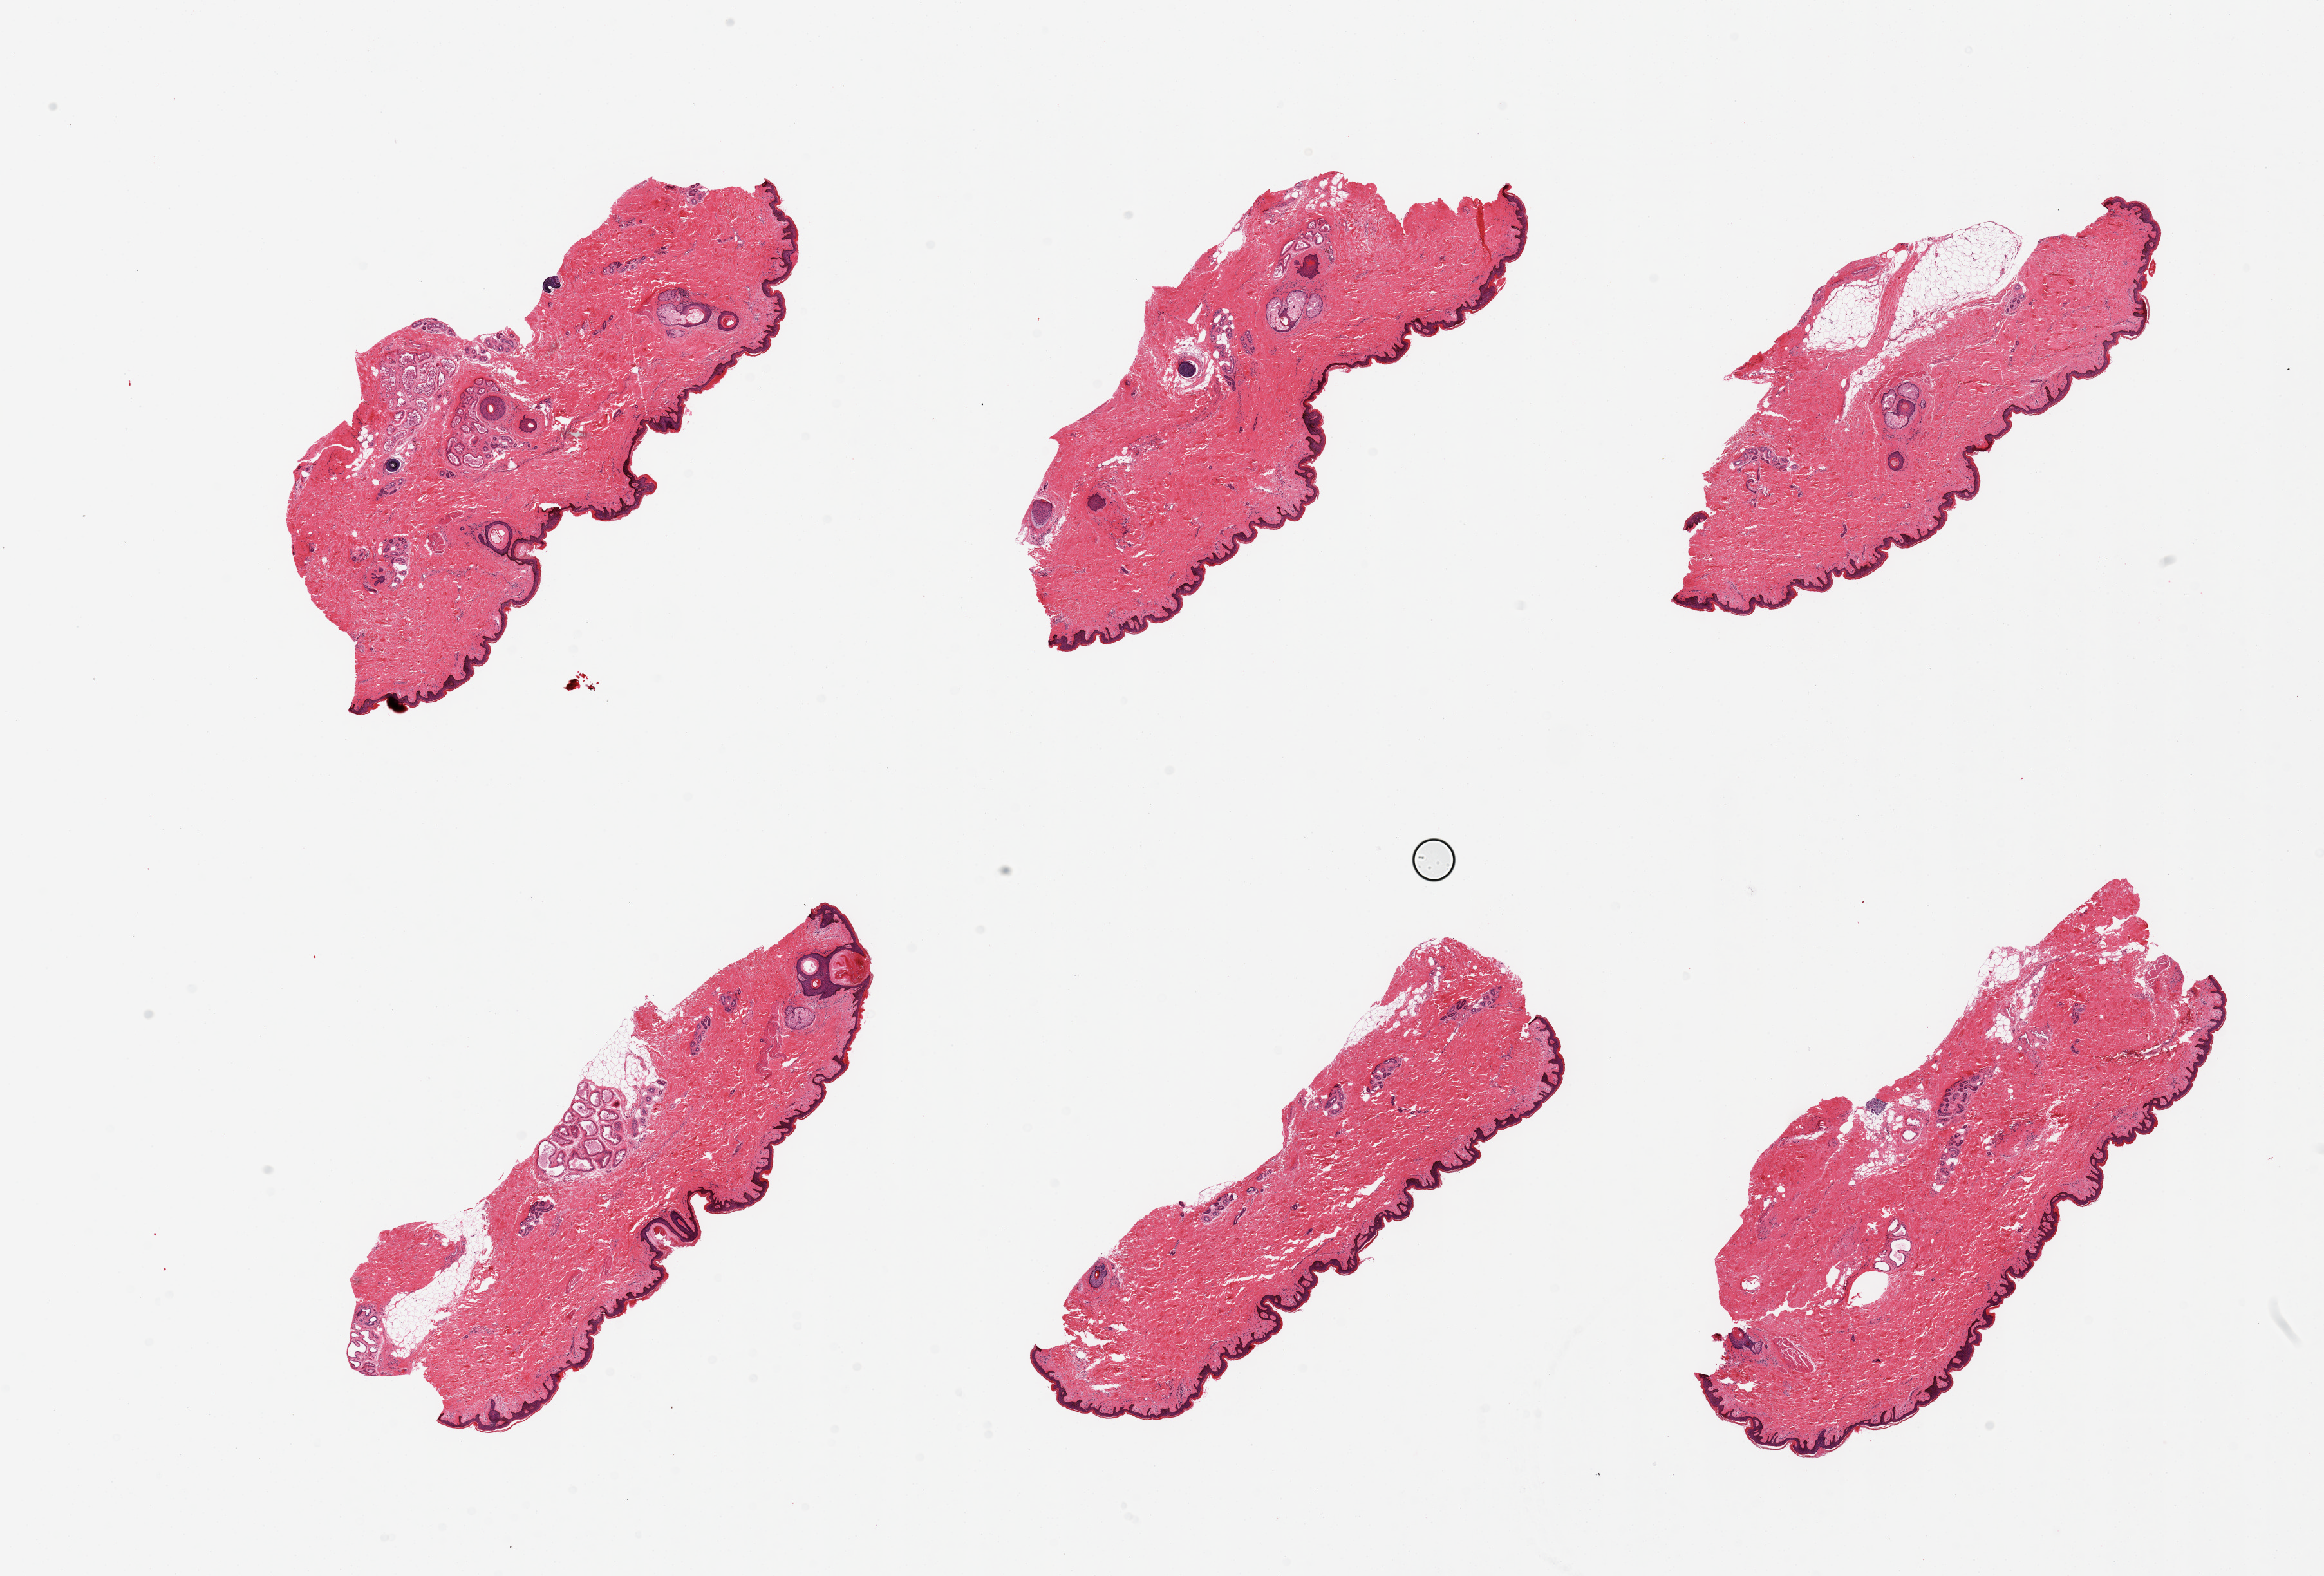
Digitized hematoxylin and eosin (H&E)-stained section, brightfield, low-resolution overview of the scanned area, about 28.5 x 19.4 mm (slide scanned at 20x), PAXgene-fixed paraffin-embedded (PFPE) section, section of skin of suprapubic region (target tissue), tissue donor sample. Donor: male.
Pathologist's review note for this sample: 6 pieces, squamous epithelium is ~40-50microns; trace nubbin adherent dermal fat.